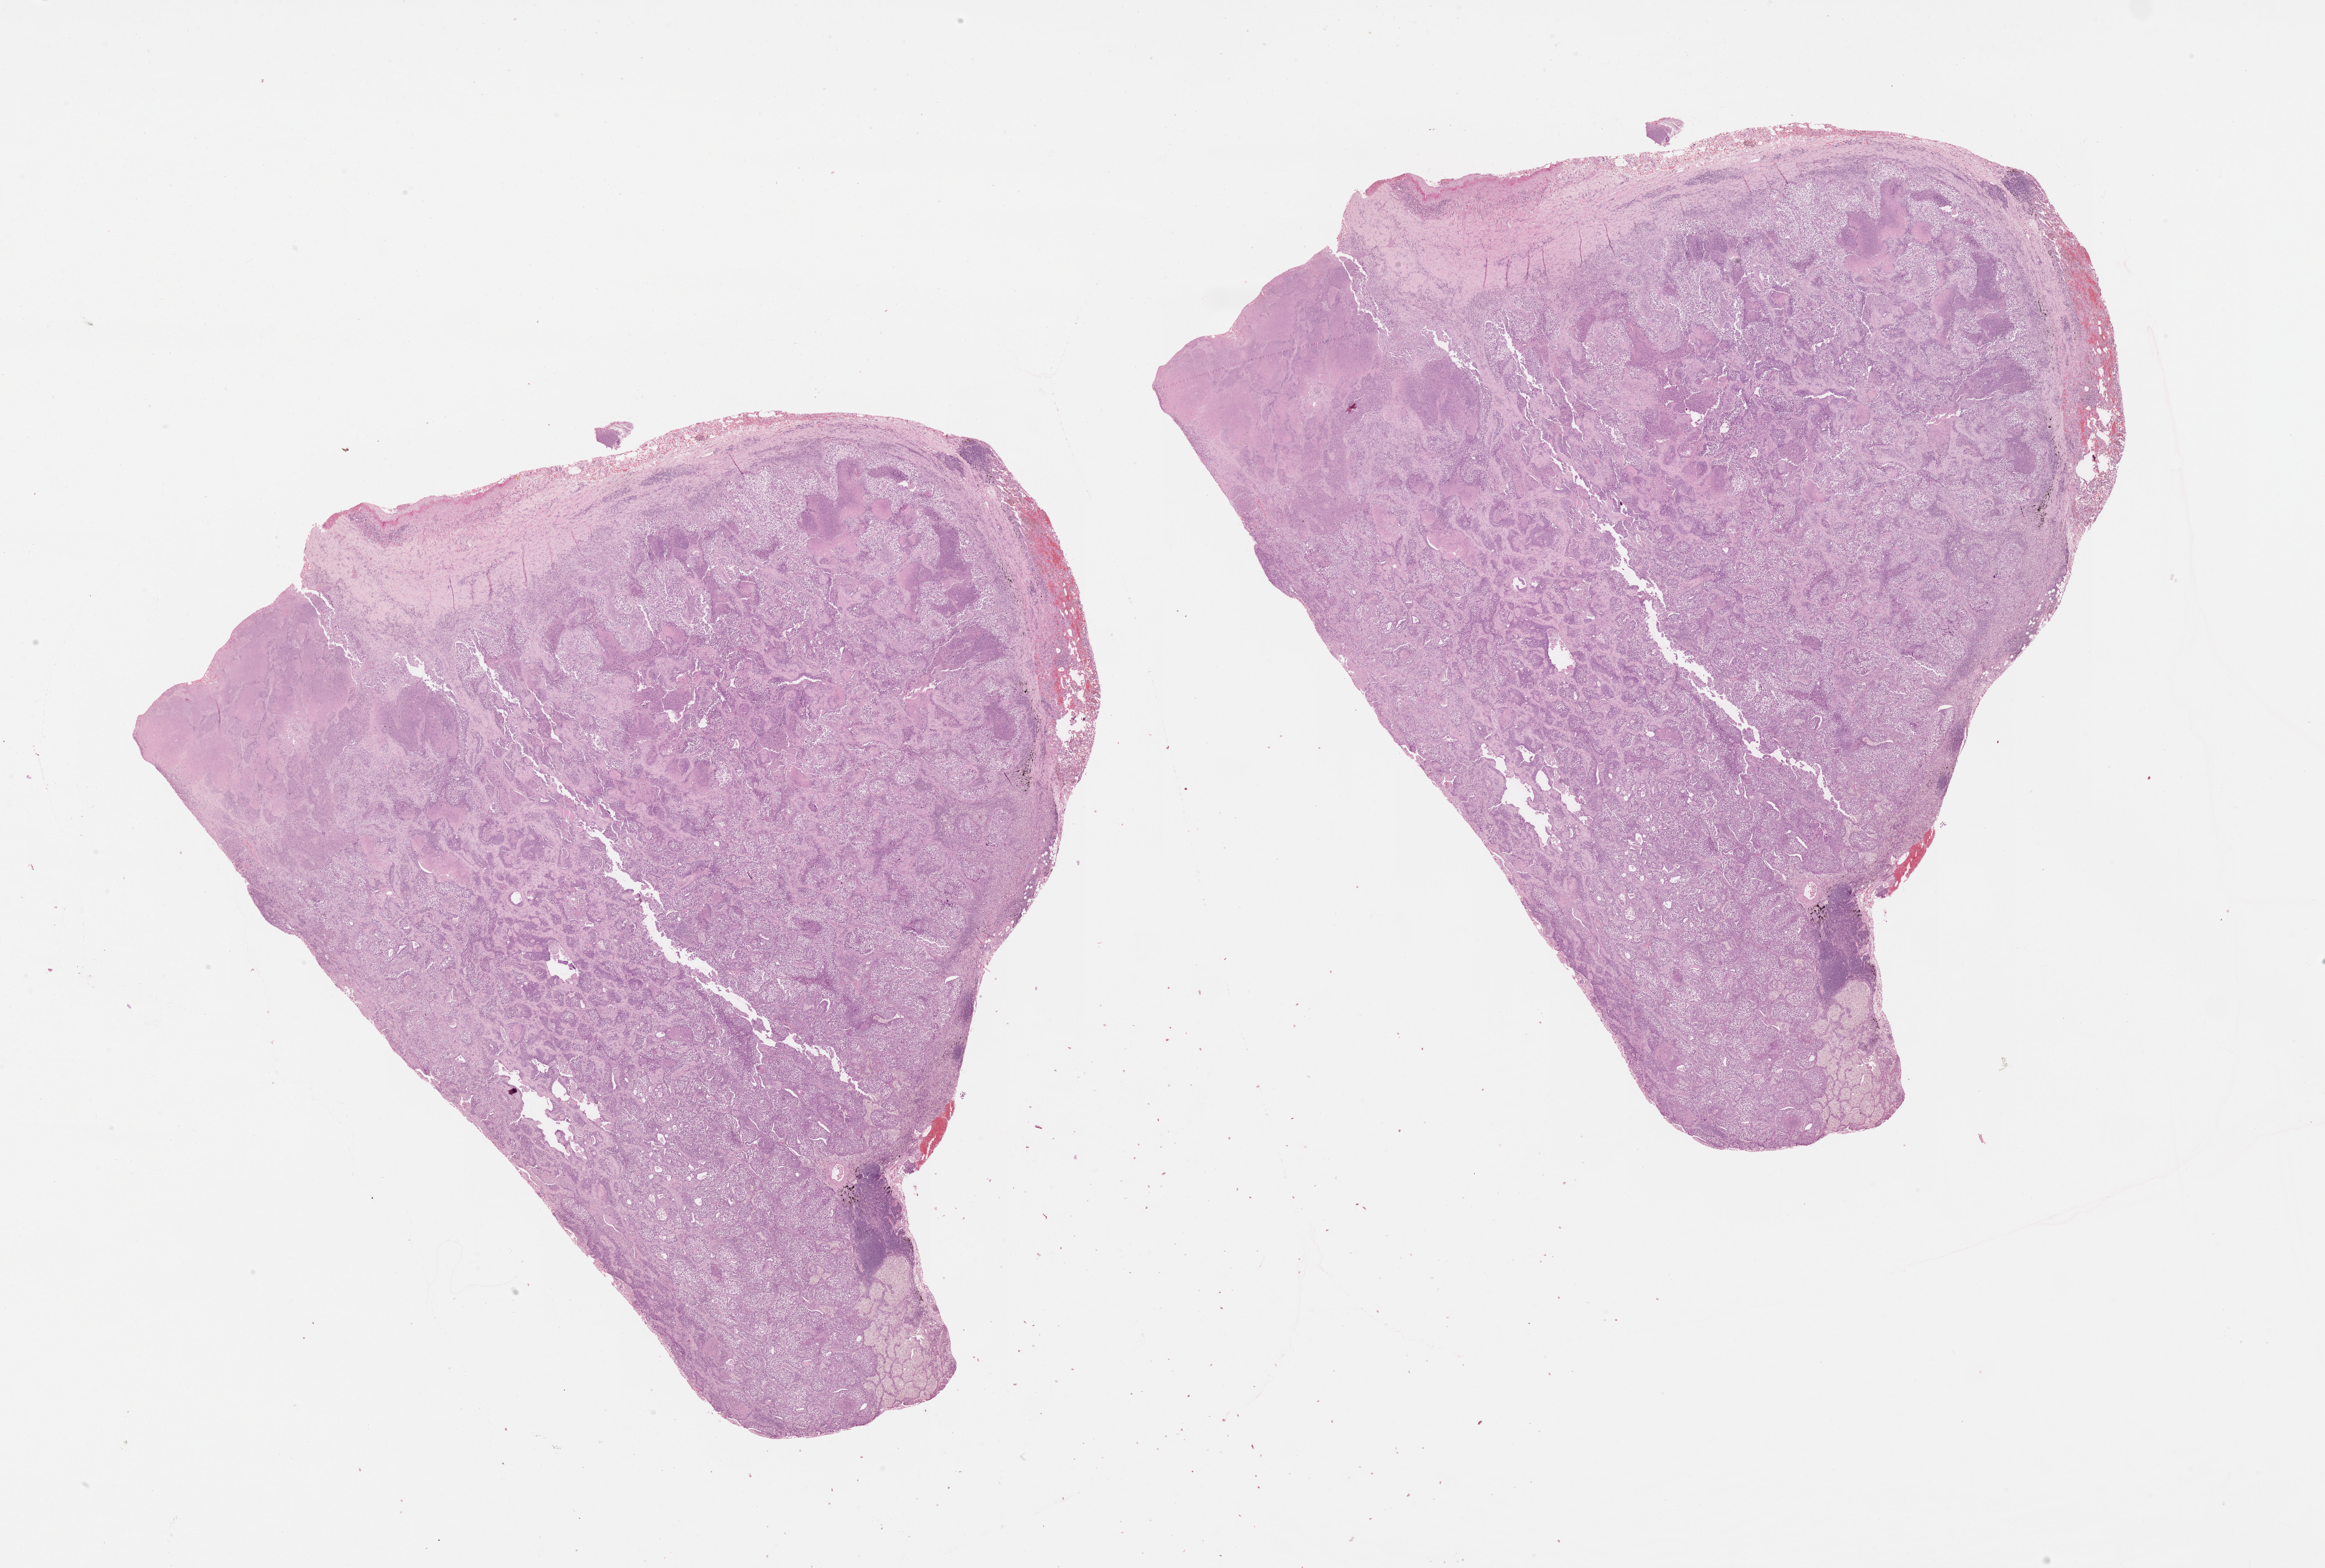
Hematoxylin and eosin (H&E) stained whole-slide image, a low-resolution overview of the entire scanned area, about 30.1 x 20.3 mm (from a 20x scan); lung, tumour tissue. 56-year-old male patient.
Patient diagnosis (cohort enrolment): squamous cell carcinoma (lung).